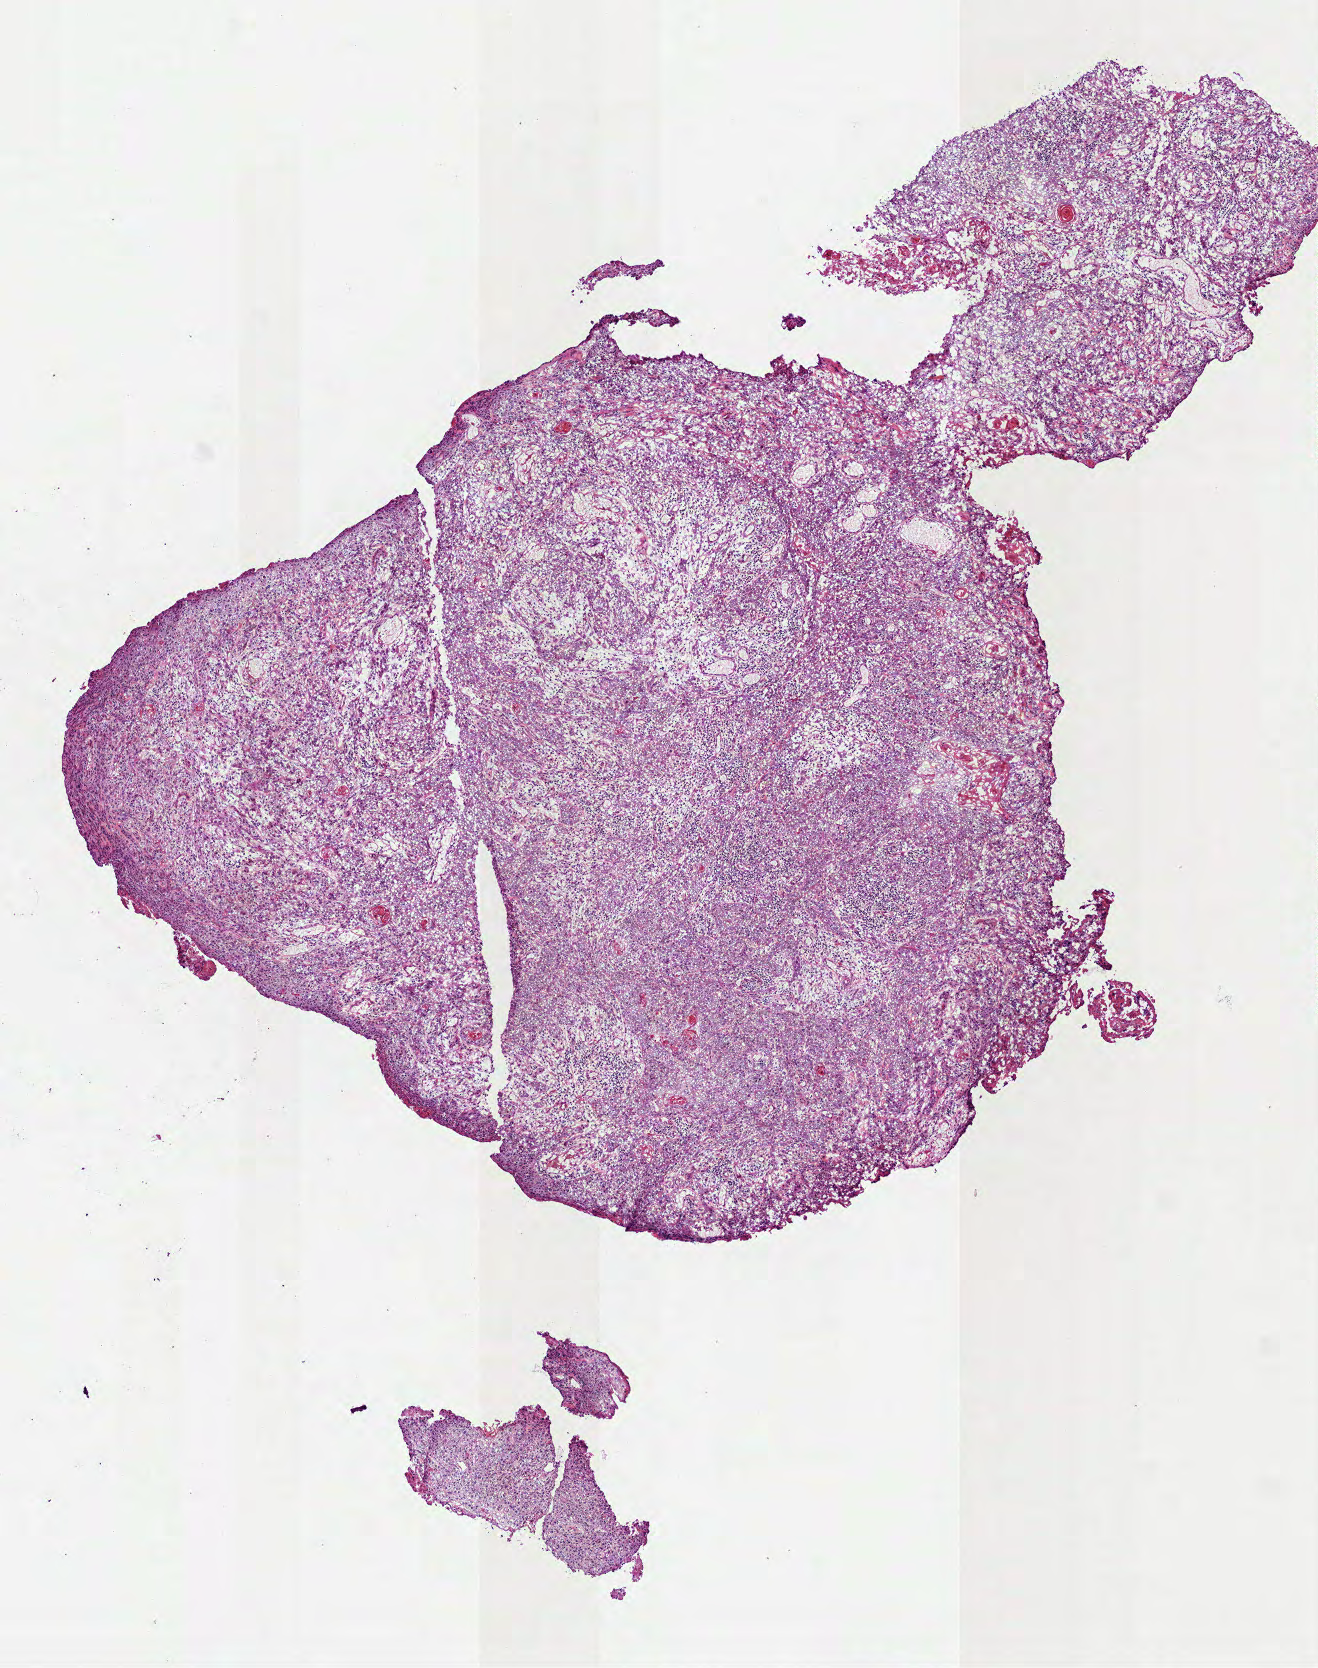
Whole-slide histology image, H&E — whole scanned area (about 5.3 x 6.7 mm, from a 40x scan) shown as a low-resolution overview. Frozen section from the top of the tissue portion. Head and neck, primary tumour sample. Male, age 54 years at initial diagnosis. Histologic grade: GX (grade cannot be assessed). Composition of this section per pathologist review: tumour cells 90%, tumour nuclei 65%, normal cells 0%, stromal cells 10%, necrosis 0%.
- laterality: right
- pathologic diagnosis: Squamous cell carcinoma, keratinizing, NOS
- AJCC pathologic stage: IVA
- TNM: T4a N1 M0